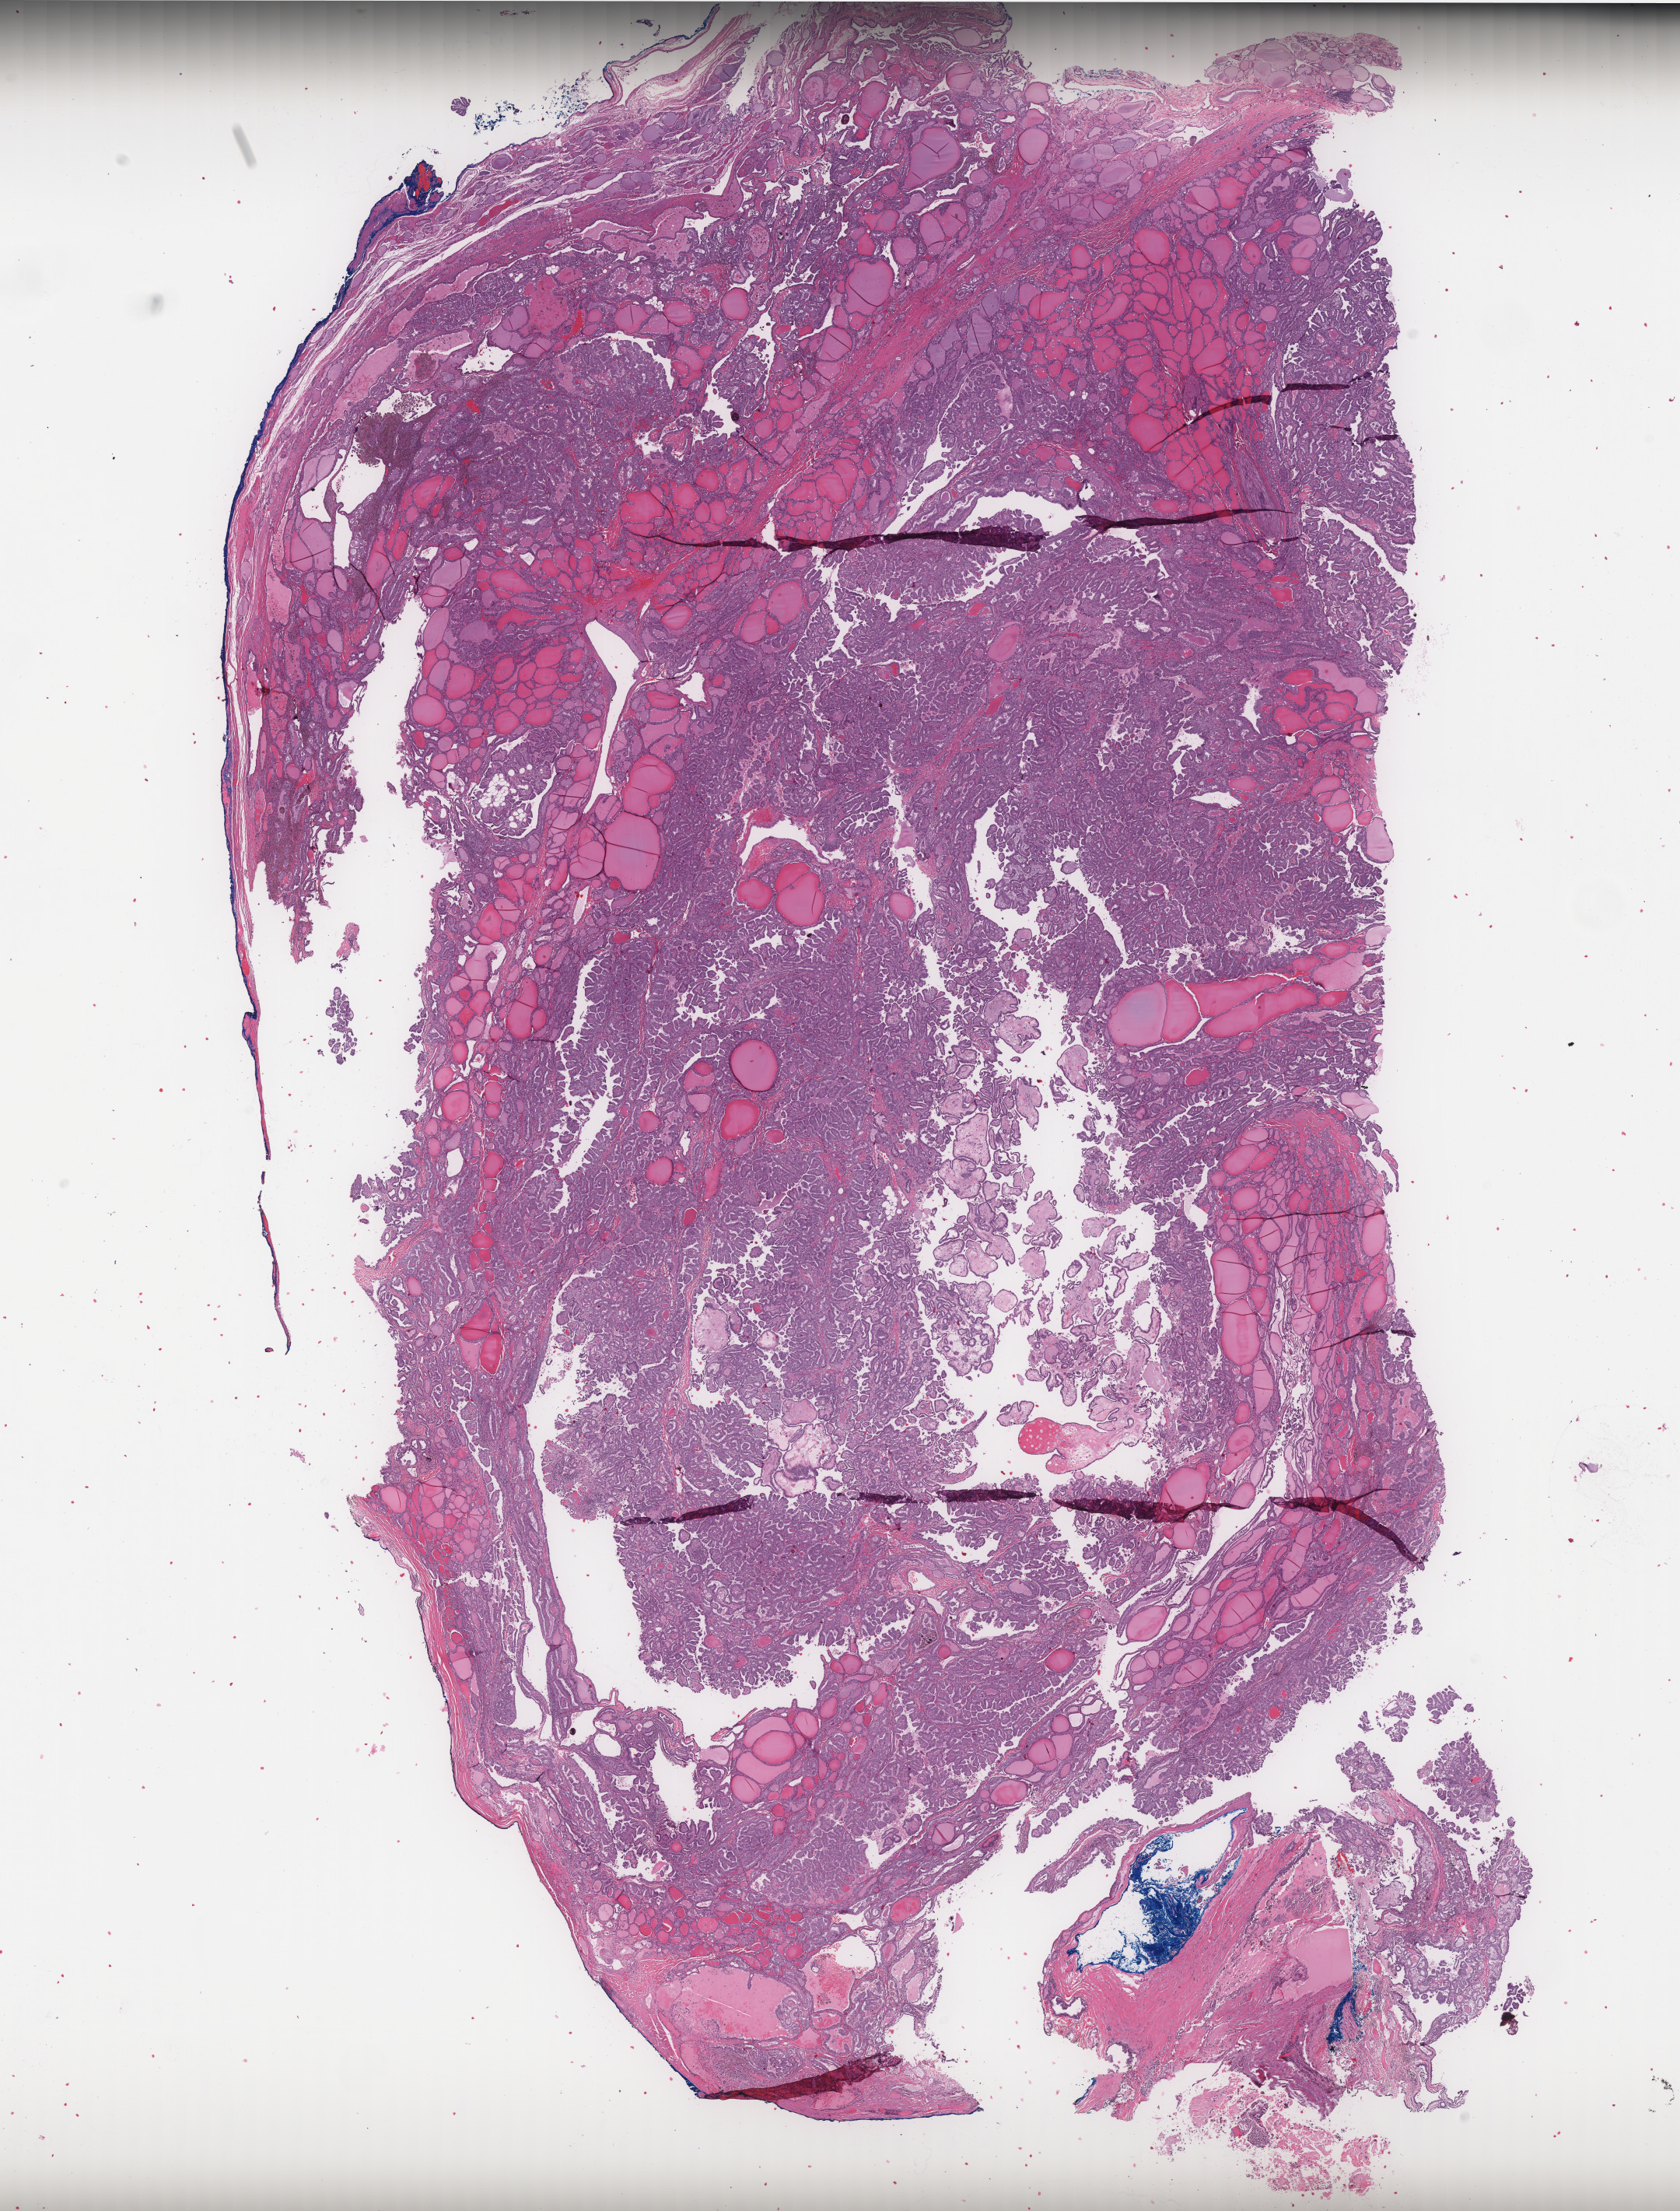
Hematoxylin and eosin (H&E) stained whole-slide image — low-resolution overview of the scanned area, about 17.3 x 22.8 mm (acquisition: 40x scan); FFPE section; thyroid, primary tumour sample. Female, age 63 years at initial diagnosis.
- diagnosis: Papillary adenocarcinoma, NOS (thyroid gland)
- AJCC pathologic stage: II (7th edition)